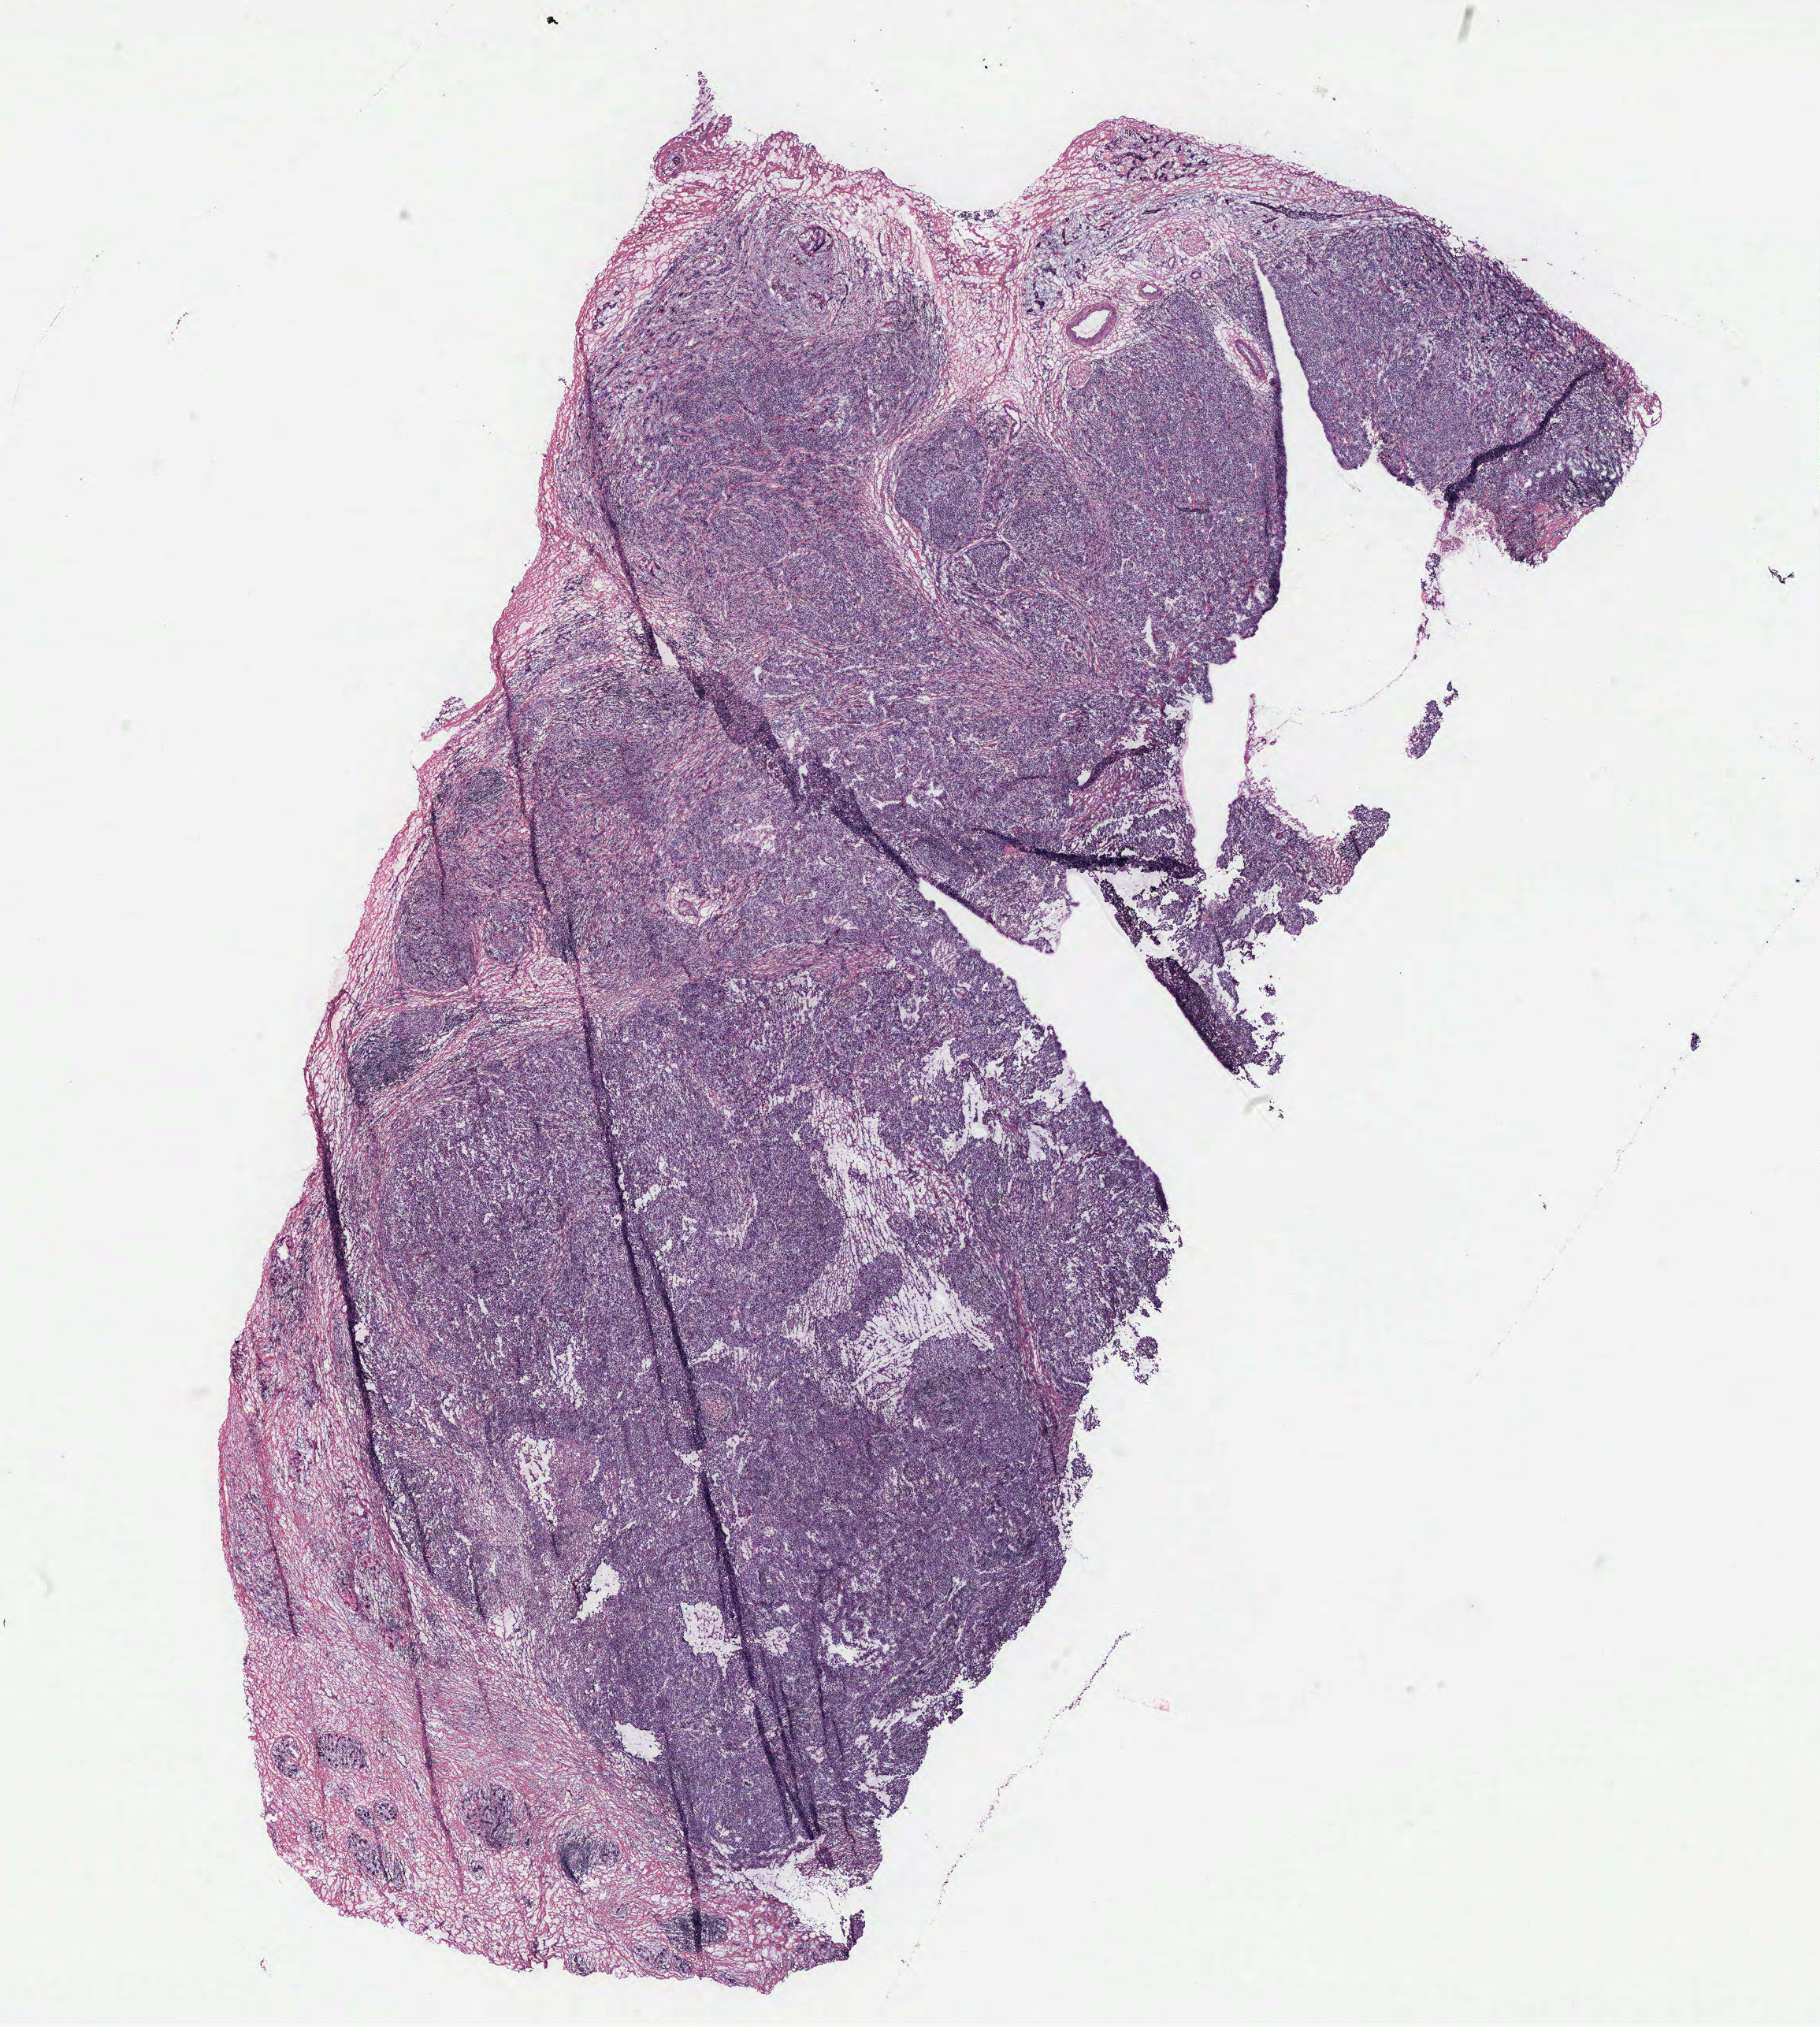
Digitized Hematoxylin and eosin (H&E) stained tissue section (whole slide), a low-resolution overview of the entire scanned area, about 18.5 x 20.6 mm. Breast, tissue type not recorded. Female, 30 y/o.
Patient diagnosis: Infiltrating duct carcinoma, NOS.